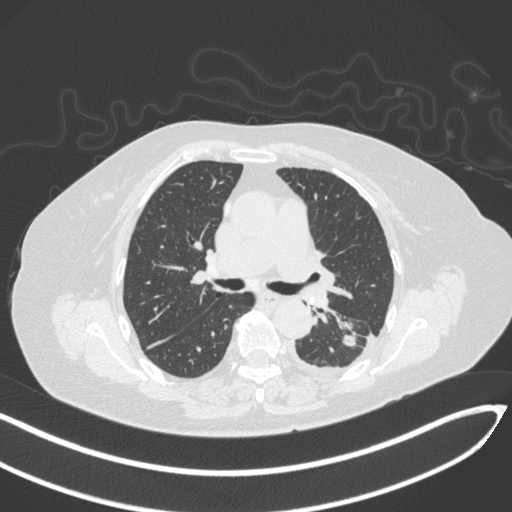
Chest CT, one axial slice. Position 191 of 270 along the scan axis. 120 kVp. Lung window (W 1500 / L -600 HU). 1 mm slice thickness. 512 × 512 image matrix. Patient: female, 76 years. Case-level facts recorded for this patient, not image findings: clinical TNM (as recorded): T1c N0 M0.
Structures marked on this image (bounding box drawn by a radiologist):
- lung tumour (recorded histology: adenocarcinoma): box from (x=340, y=334) to (x=357, y=348) px